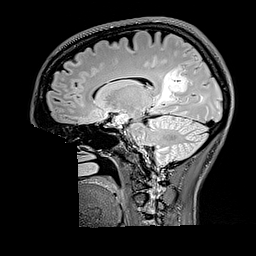
Brain MRI from a brain-tumour surgery series, one sagittal slice. Position 100 of 176 along the scan axis. T2 FLAIR. 1 mm slice thickness. 256 × 256 image matrix, field of view 256 × 256 mm. Case-level facts recorded for this patient, not image findings: histopathology: Oligodendroglioma; WHO grade: 2; IDH mutation: yes; tumour location: Right Parietal.
Structures marked on this image (expert manual segmentation):
- tumour: bounding box <159,65,188,103> (left, top, right, bottom; pixels)